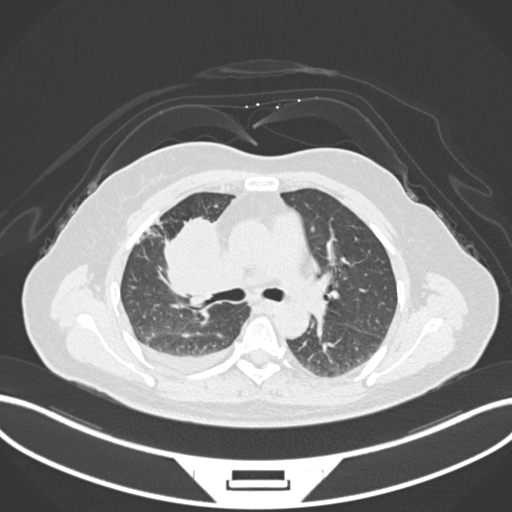
Chest CT, one axial slice. Position 91 of 172 along the scan axis. Reconstruction kernel B30f. 120 kVp. Lung window (W 1500 / L -600 HU). 512 × 512 image matrix, field of view 400 × 400 mm. Patient: female, 52 years. From the clinical record (not read from this slice): clinical TNM (as recorded): T3 N1 M1.
Annotated regions visible in this slice (rectangle marked by the reading radiologist):
- lung tumour (recorded histology: adenocarcinoma): bounding box <160,214,222,306> (left, top, right, bottom; pixels)